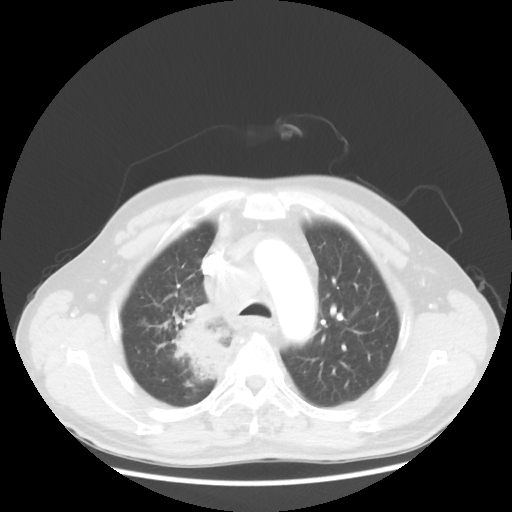
Chest CT, one axial slice. Slice 93 of 124 in the series (ordered by position). Lung window (W 1500 / L -600 HU). 5 mm slice thickness. 512 × 512 image matrix. Patient: male, 64 years. Case-level facts recorded for this patient, not image findings: clinical TNM (as recorded): T3 N3 M0; histopathological grade: G3.
Structures marked on this image (bounding box drawn by a radiologist):
- lung tumour (recorded histology: small cell carcinoma): bounding box (x1, y1, x2, y2) in pixels: (170, 298, 239, 395)